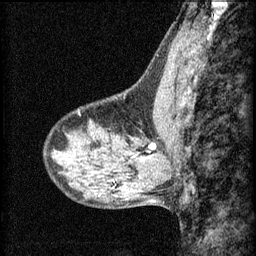
Breast MRI (dynamic contrast-enhanced), one sagittal slice. Slice 22 of 60 in the series (ordered by position). 3 images stored at this slice position (order not interpretable as contrast timing). 1.5 T. TE 4.2 ms, TR 8.2 ms. 2 mm slice thickness. 256 × 256 image matrix, field of view 180 × 180 mm. Female patient, age 40 years.
Outlined on this slice (semi-automatic segmentation, software-assisted and operator-edited):
- analysis volume of interest (the breast-tissue region the enhancement analysis was run in; not a lesion): bounding box [x1, y1, x2, y2] px = [104, 116, 159, 165]
- tumour enhancement mask (voxels above the 70 % enhancement threshold inside the analysis volume of interest): [132, 144, 155, 159]